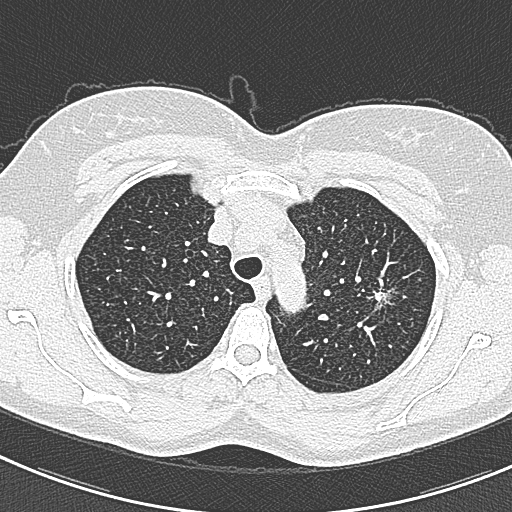
Low-dose screening chest CT, axial slice, baseline annual screen, lung window (W 1500 / L -600 HU). Female participant, aged 57 years at enrolment. Current smoker at enrolment.
- Lesion marked by an expert reader, box from (x=363, y=274) to (x=413, y=321) px.
- The screening reader recorded 2 non-calcified nodules or masses ≥4 mm on this exam; which of them this box marks is not recorded.
- Official screen result: positive, change unspecified: nodule(s) >= 4 mm or enlarging nodule(s), mass(es), or other non-specific abnormalities suspicious for lung cancer.
- Participant outcome: lung cancer diagnosed 198 days after this screen — adenocarcinoma, NOS, left upper lobe, well differentiated (G1), stage IA (AJCC 6th edition), 10 mm at pathology.